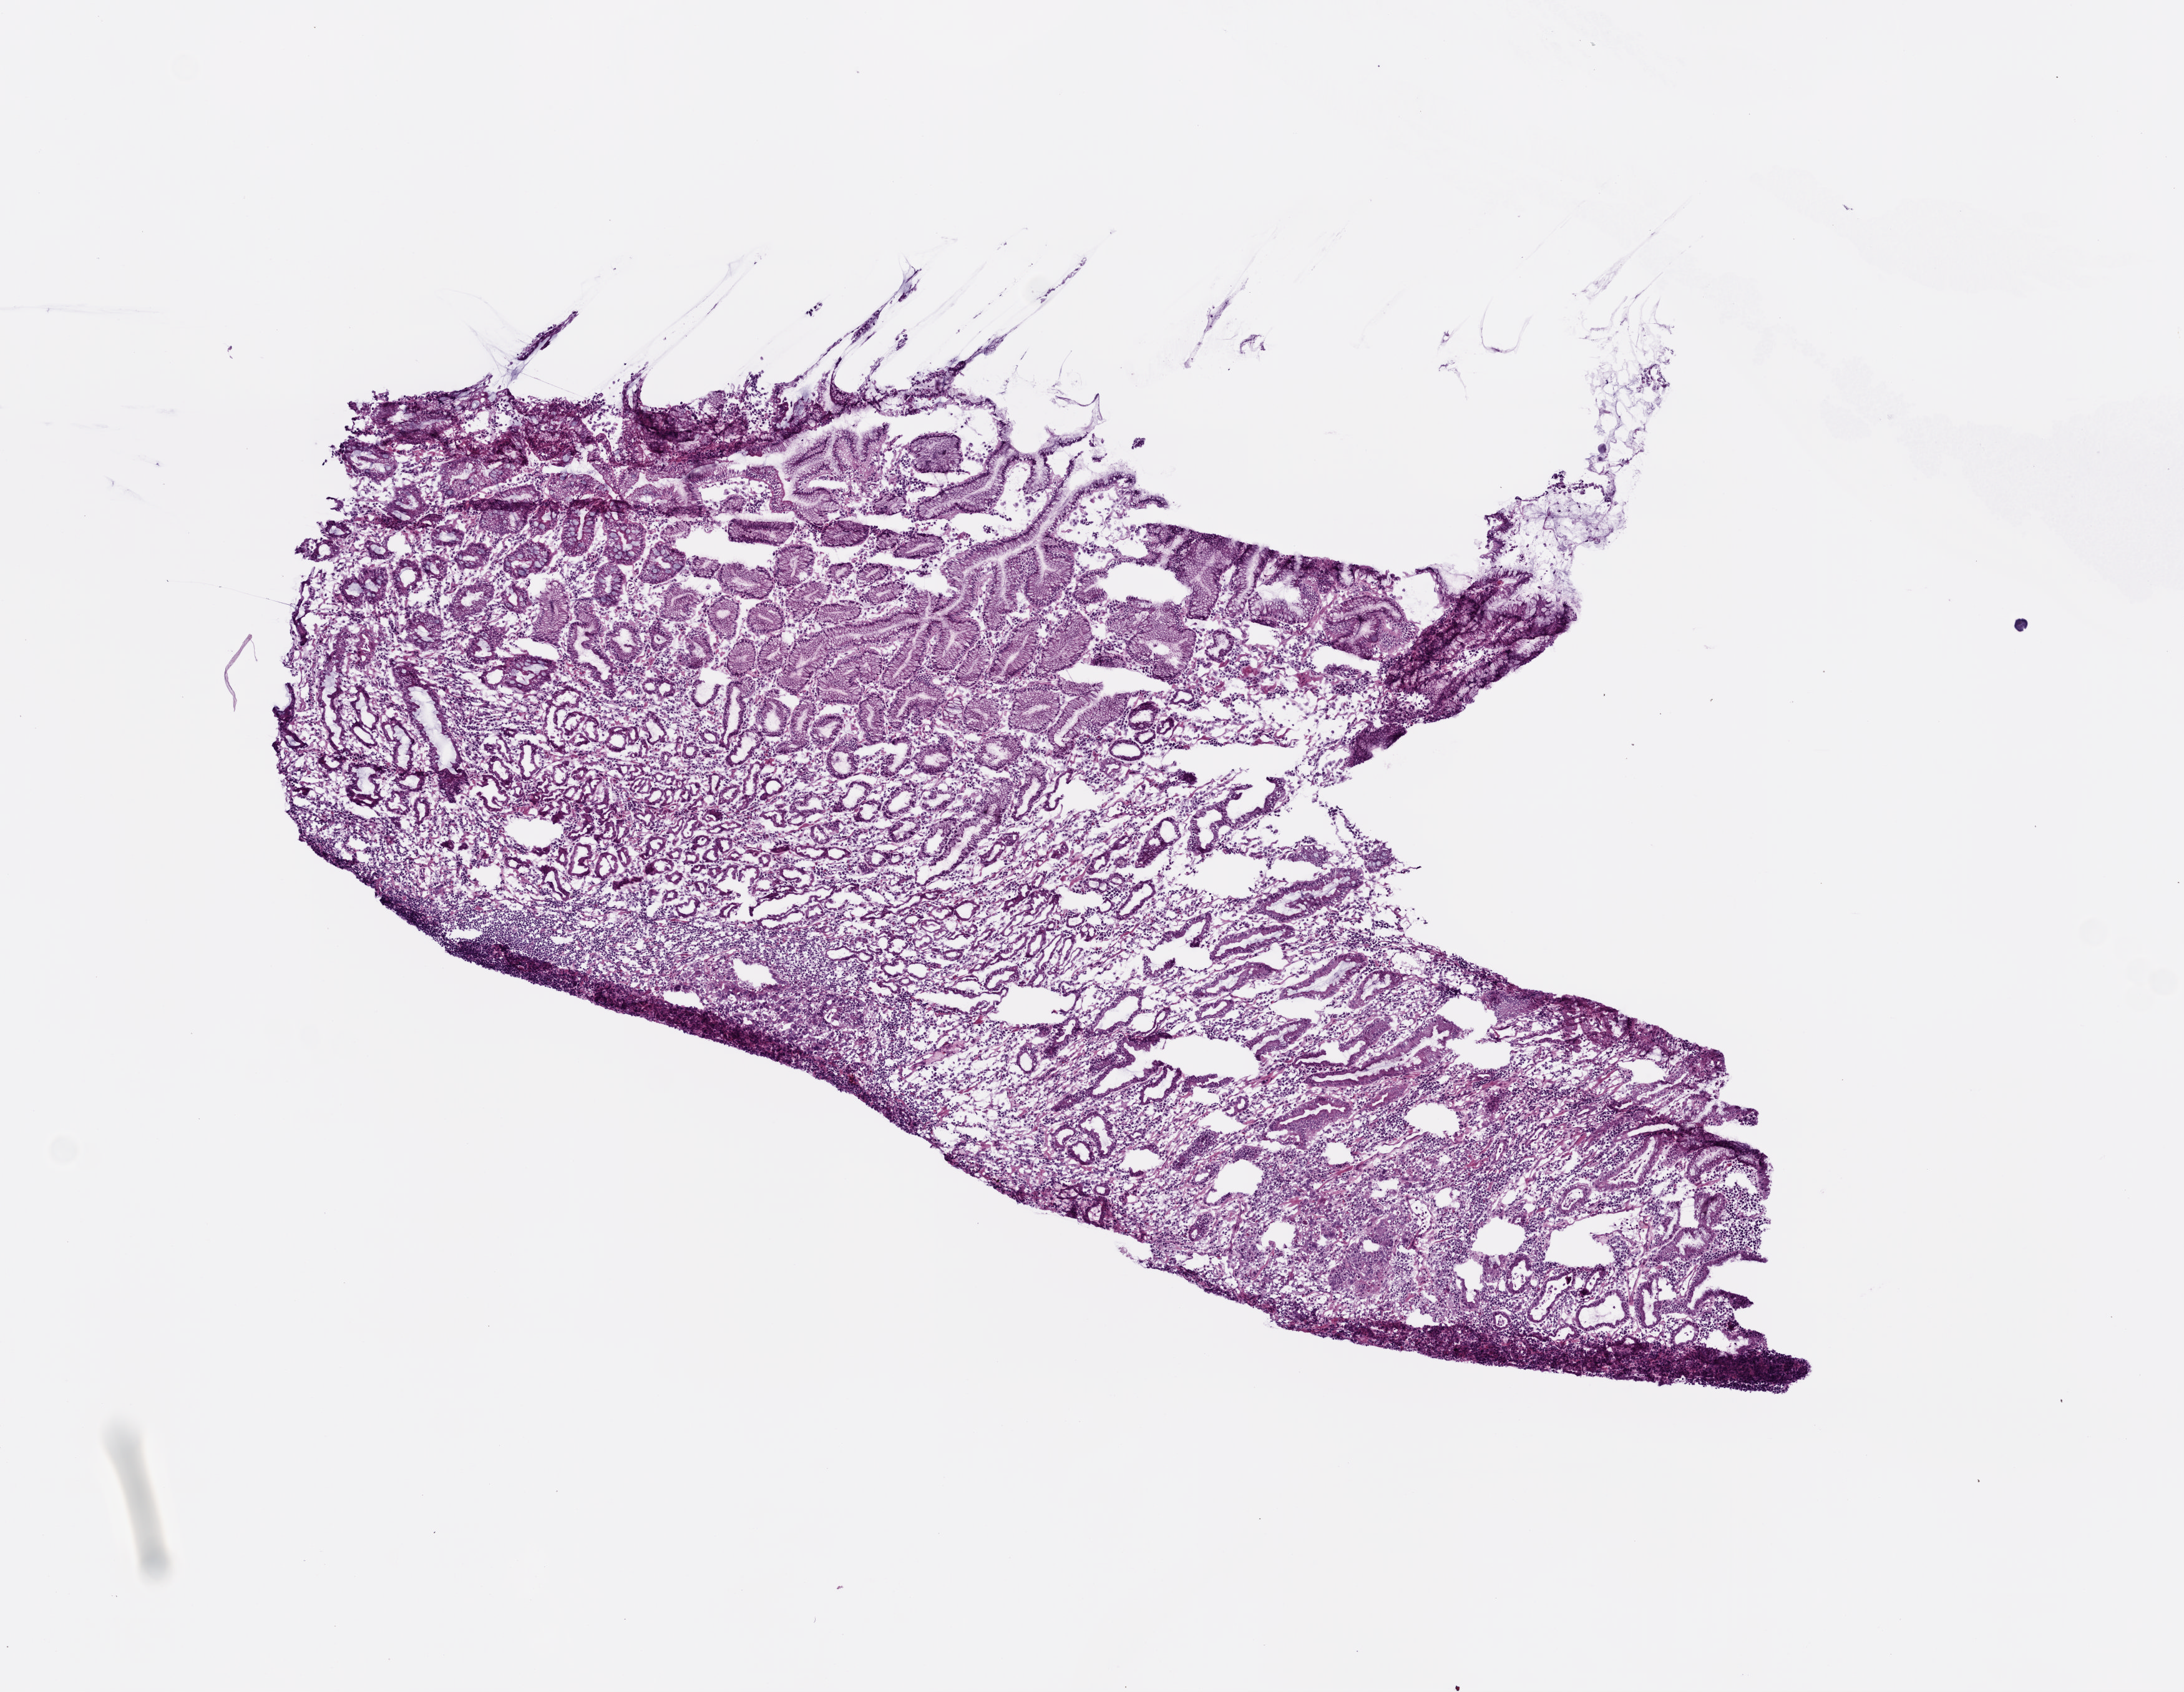
Whole-slide histology image, H&E — low-resolution overview of the scanned area, about 7.0 x 5.4 mm (slide scanned at 20x). Frozen section from the top of the tissue portion. Primary tumour sample from the stomach. Male, age 68 years at initial diagnosis. Pathologist review of this section (percent, as recorded): tumour cells 55%, tumour nuclei 60%.
Diagnosis: Adenocarcinoma, intestinal type (body of stomach).